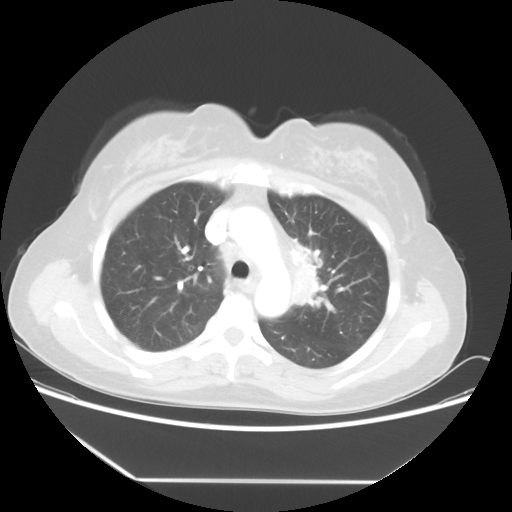
Chest CT, one axial slice; slice 37 of 52 in the series (ordered by position); 100 kVp; lung window (W 1500 / L -600 HU); 5 mm slice thickness; 512 × 512 image matrix, field of view 390 × 390 mm. Patient: female, 50 years. From the clinical record (not read from this slice): clinical TNM (as recorded): T2 N3 M0.
Outlined on this slice (rectangle marked by the reading radiologist):
- lung tumour (recorded histology: adenocarcinoma): bounding box <278,230,329,318> (left, top, right, bottom; pixels)